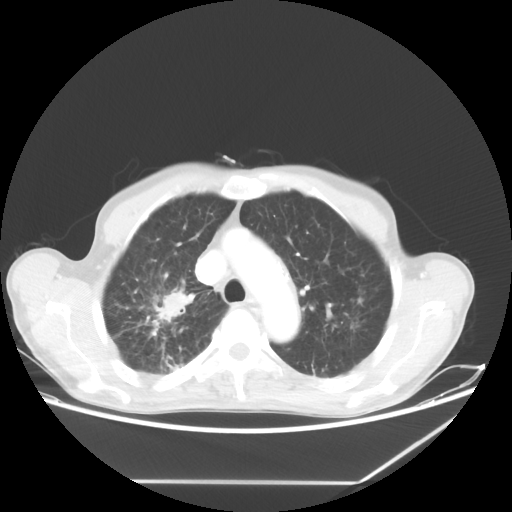
Chest CT, one axial slice; slice 48 of 65 in the series (ordered by position); reconstruction kernel STANDARD; 80 kVp; lung window (W 1500 / L -600 HU); 512 × 512 image matrix. Patient: male, 68 years. From the clinical record (not read from this slice): clinical TNM (as recorded): T3 N3 M0.
Outlined on this slice (bounding box drawn by a radiologist):
- lung tumour (recorded histology: adenocarcinoma): box from (x=142, y=283) to (x=199, y=327) px